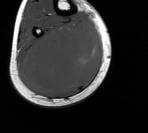
MRI of an extremity soft-tissue mass, one axial slice; position 52 of 76 along the scan axis; MR volume resampled by the dataset authors to the PET/CT grid (not the native acquisition matrix); 3.27 mm slice thickness; 148 × 133 image matrix. Male patient. From the clinical record (not read from this slice): histological type: liposarcoma - round cell; grade: high; site of the primary tumour: right calf.
Outlined on this slice (expert contour drawn on MRI and transferred to this co-registered scan by the dataset authors):
- gross tumour volume (mass): bounding box <20,21,100,95> (left, top, right, bottom; pixels)